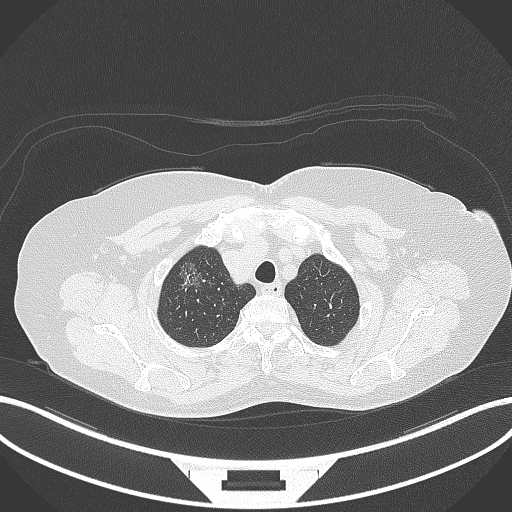
Chest CT, one axial slice. Position 304 of 365 along the scan axis. 120 kVp. Lung window (W 1500 / L -600 HU). 512 × 512 image matrix, field of view 400 × 400 mm. Patient: female, 62 years. From the clinical record (not read from this slice): clinical TNM (as recorded): T1c N0 M0.
Annotated regions visible in this slice (rectangle marked by the reading radiologist):
- lung tumour (recorded histology: adenocarcinoma): bounding box (x1, y1, x2, y2) in pixels: (174, 257, 209, 300)